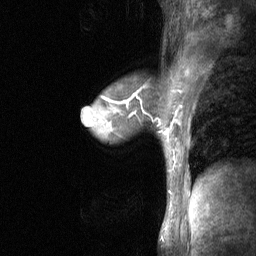
Breast MRI (dynamic contrast-enhanced), one sagittal slice. Position 42 of 64 along the scan axis. Dynamic contrast-enhanced study with each time point stored as its own series, time point 2 of 3 at this slice position (early post-contrast, ordered by acquisition time). 1.5 T. TE 4.8 ms, TR 27 ms. 2 mm slice thickness. 256 × 256 image matrix, field of view 200 × 200 mm. Female patient, age 44 years. Case-level facts recorded for this patient, not image findings: setting: breast cancer imaged before/during neoadjuvant chemotherapy; receptor status: HR-positive, HER2-negative.
Structures marked on this image (semi-automatically segmented with operator editing):
- analysis volume of interest (the breast-tissue region the enhancement analysis was run in; not a lesion): bounding box <140,109,180,148> (left, top, right, bottom; pixels)
- tumour enhancement mask (voxels above the 90 % enhancement threshold inside the analysis volume of interest): <143,111,175,134>